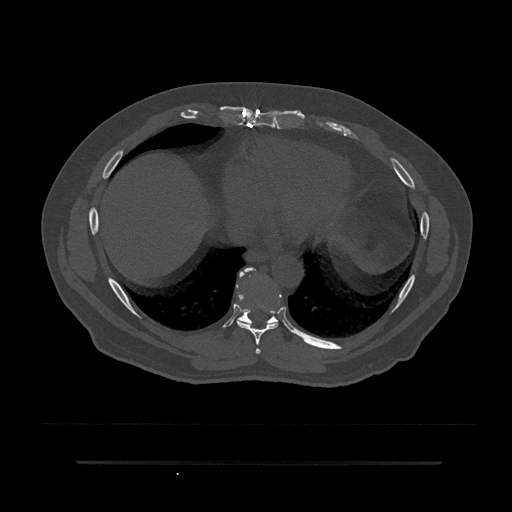
CT including the spine, one axial slice; position 408 of 797 along the scan axis; 120 kVp; bone window (W 1800 / L 400 HU); 0.5 mm slice thickness; 512 × 512 image matrix. Male patient, age 59 years. From the clinical record (not read from this slice): primary cancer: bile ducts; vertebrae with lytic lesions (as recorded): T10.
Outlined on this slice (semi-automatic segmentation, software-assisted and operator-edited):
- T7 vertebra: bounding box <255,348,261,354> (left, top, right, bottom; pixels)
- T8 vertebra: <236,268,279,354>
- T9 vertebra: <237,267,280,325>